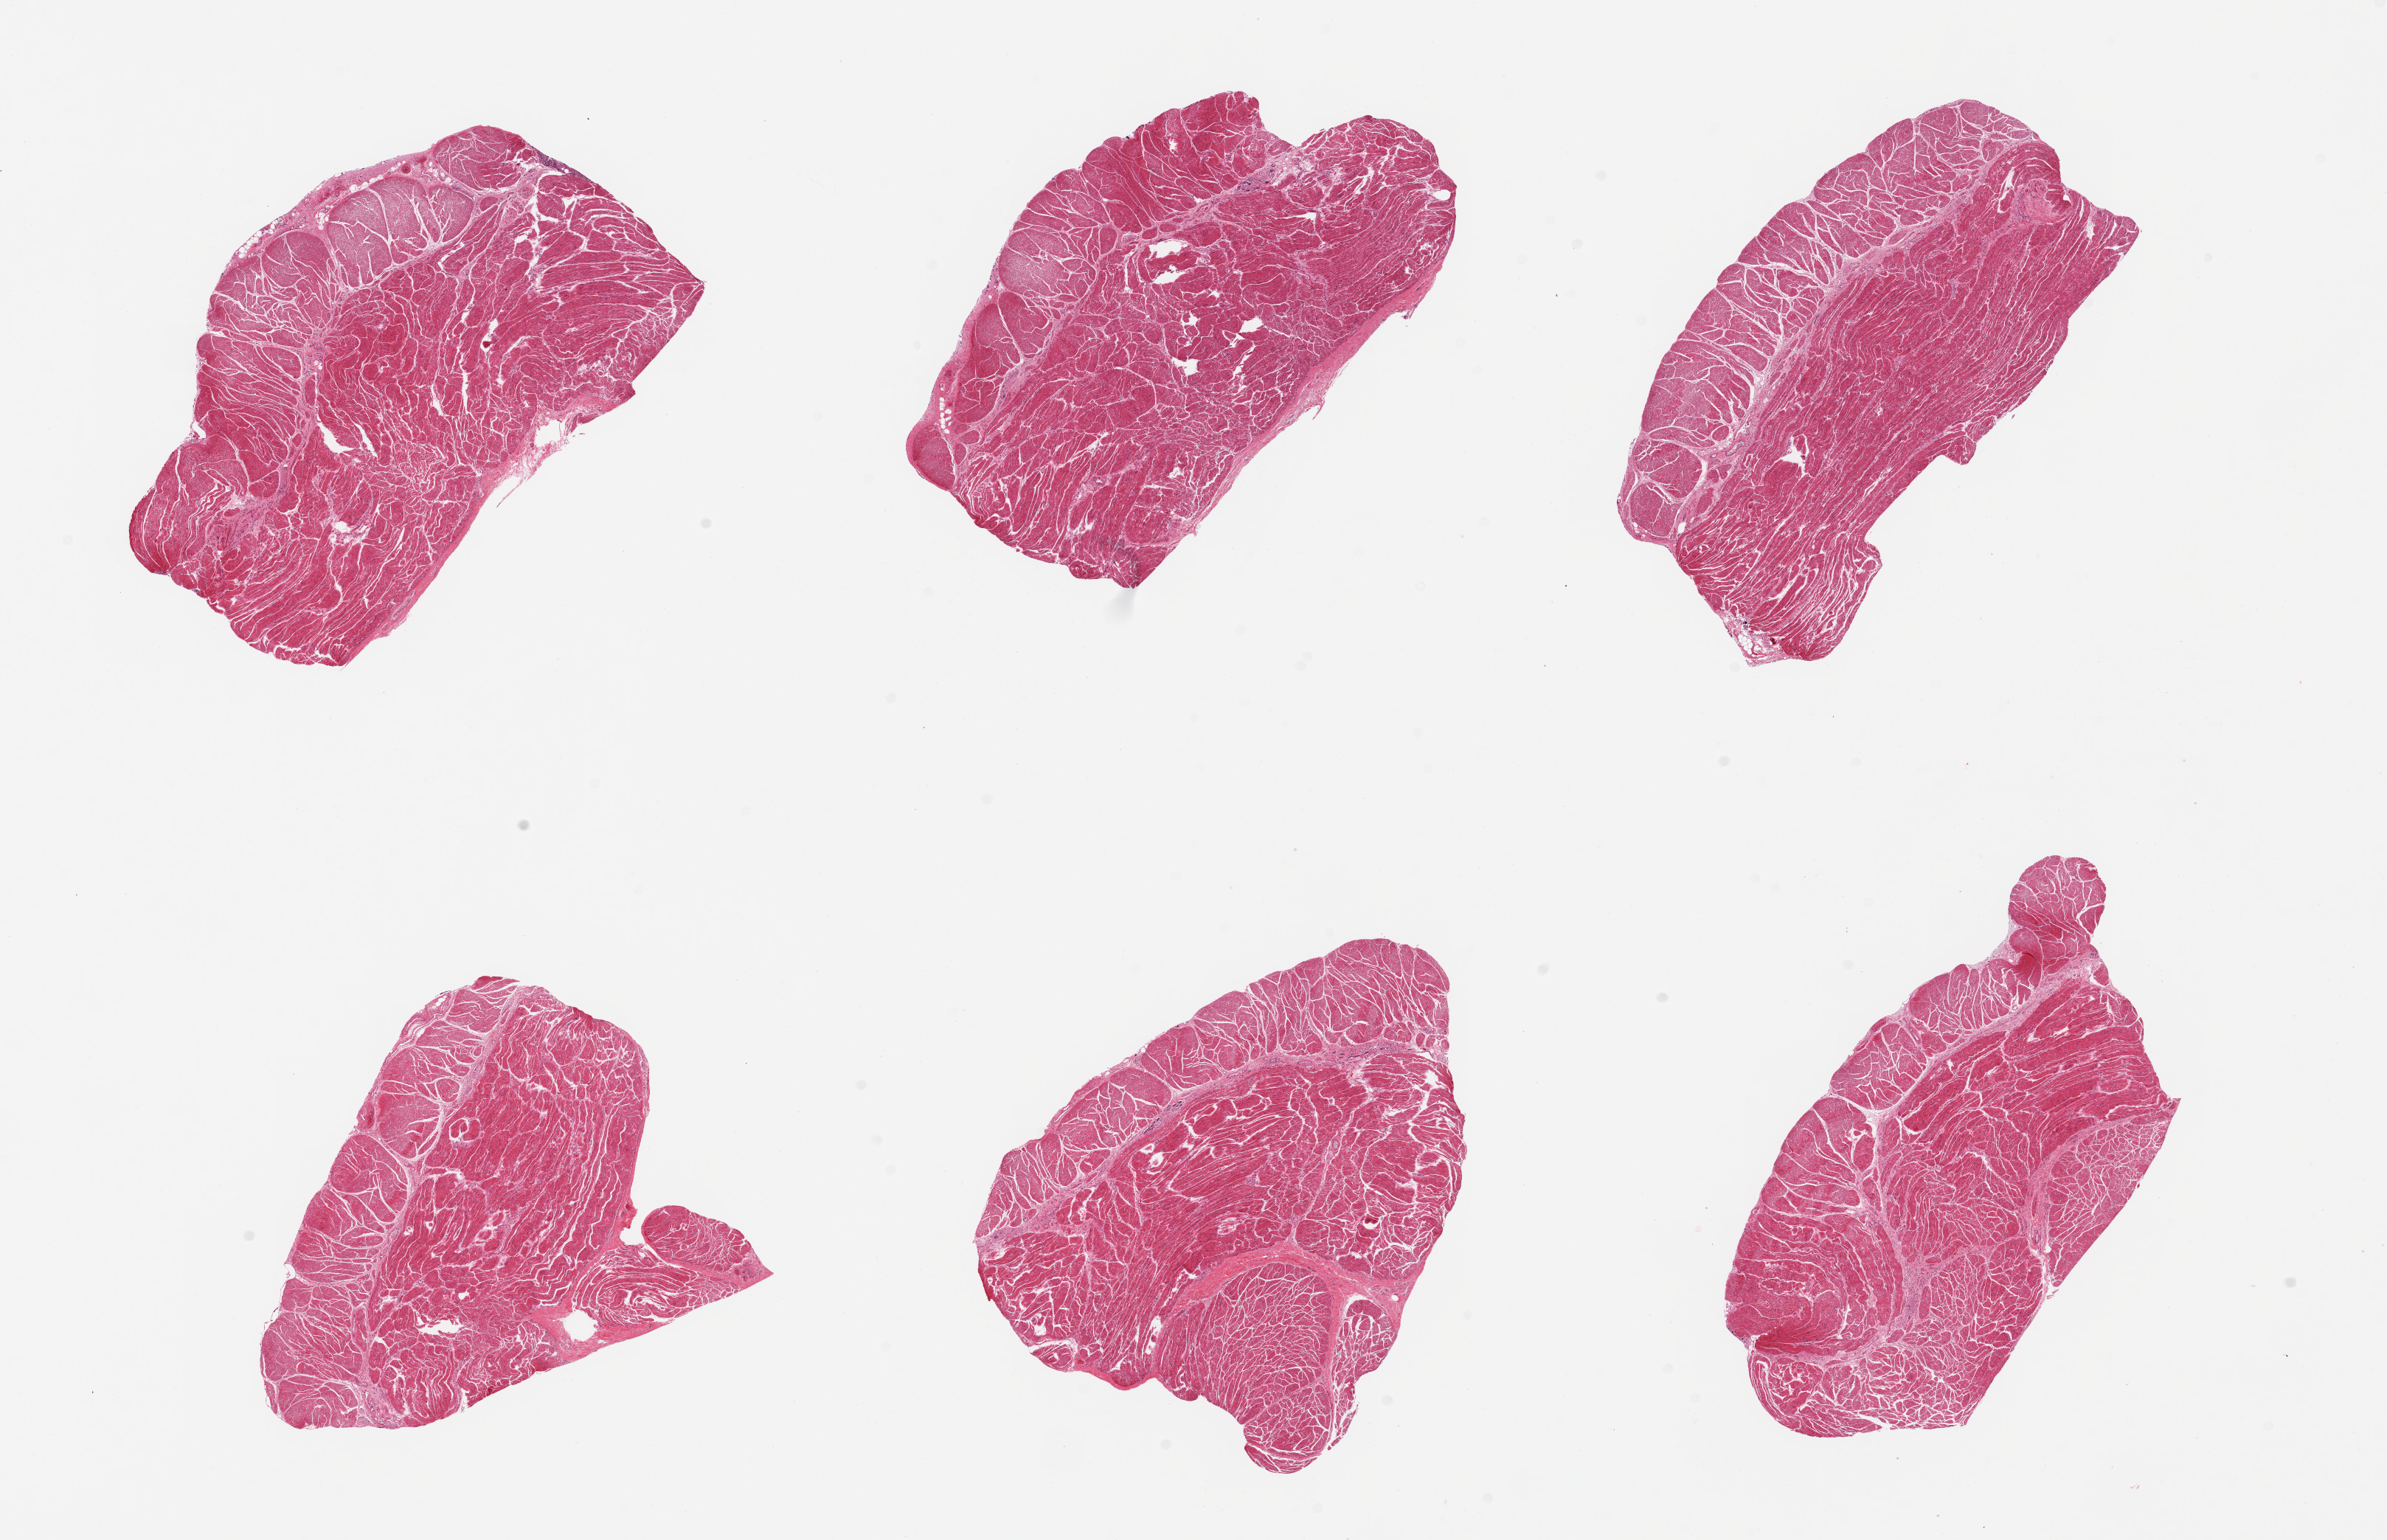
Haematoxylin and eosin whole-slide image — shown as a low-resolution overview of the whole scanned area (about 25.6 x 16.5 mm); PAXgene-fixed paraffin-embedded (PFPE) section; sampled site (target tissue): esophageal muscle; donor tissue sample.
• reviewer comment on this tissue sample: 6 pieces, all muscularis, good specimen